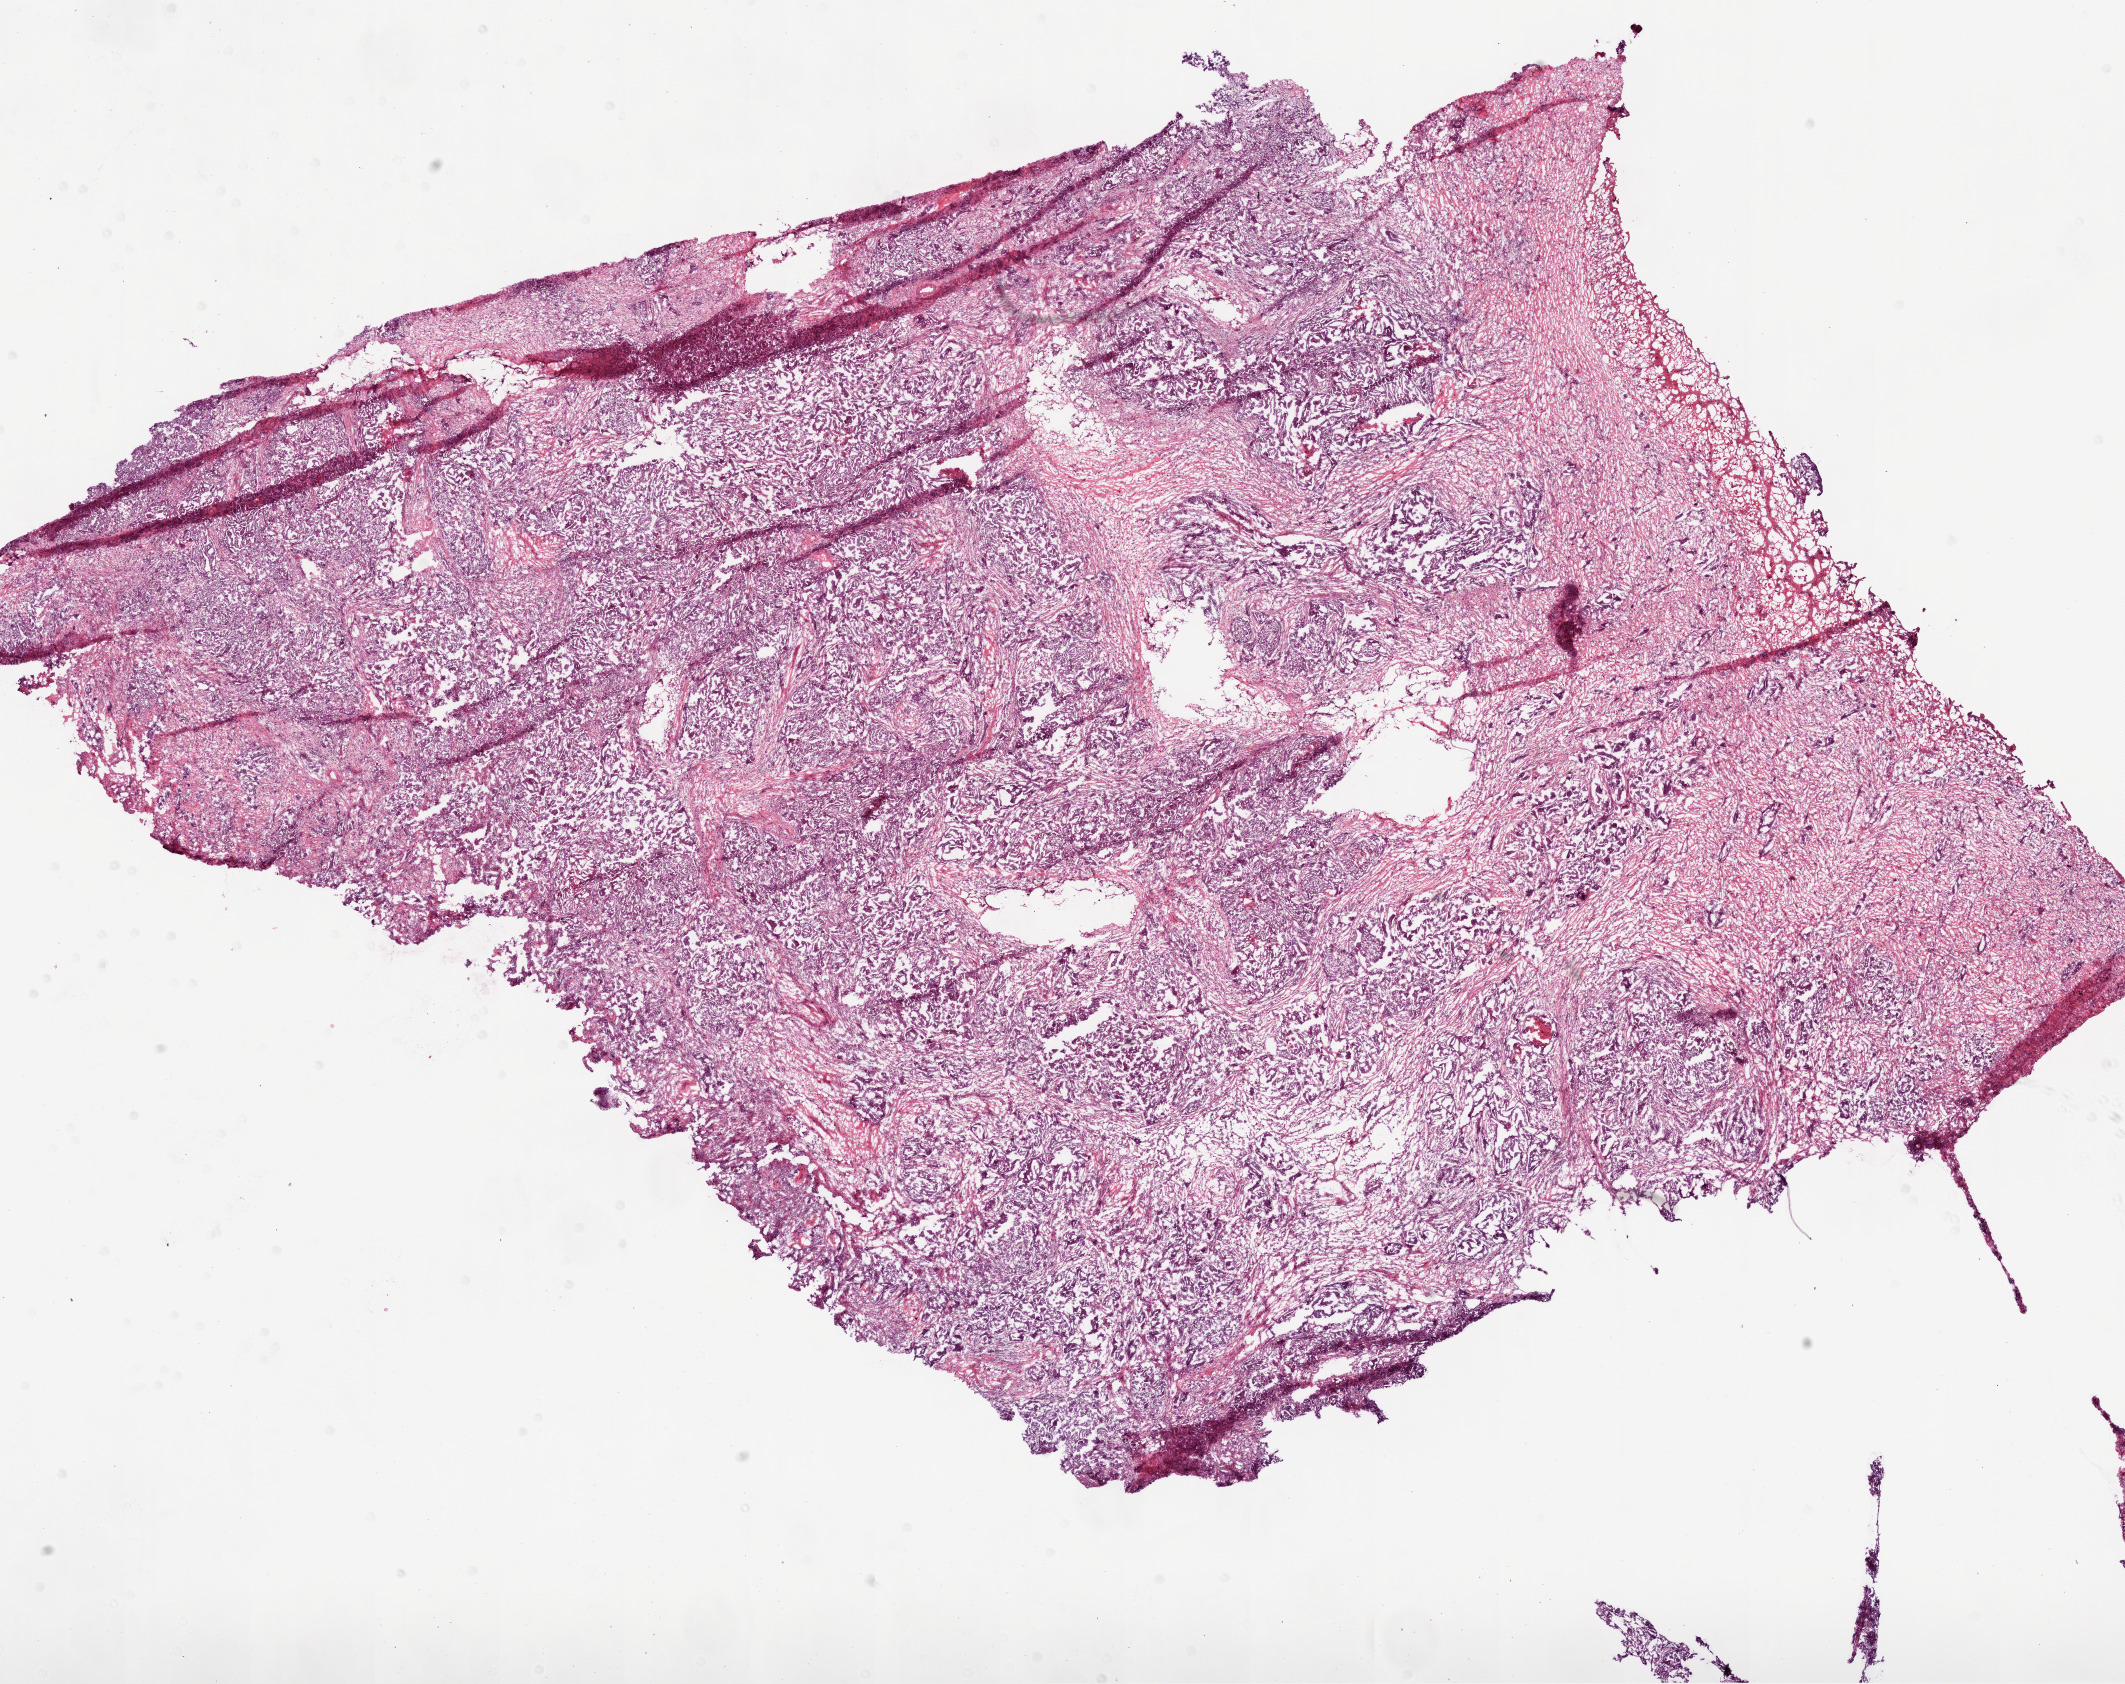
Digitized Hematoxylin and eosin (H&E) stained tissue section (whole slide) — a low-resolution overview of the entire scanned area, about 17.1 x 13.5 mm. Frozen section from the bottom of the tissue portion. Sample: primary tumour, ovary. Patient: female, age at initial diagnosis 69 years. Histologic grade: G3 (poorly differentiated). Slide review estimates, as recorded: tumour cells 80%, tumour nuclei 90%, normal cells 0%, stromal cells 20%, necrosis 0%.
FIGO stage: IIIC. Laterality: bilateral. Diagnosis: Serous cystadenocarcinoma, NOS.